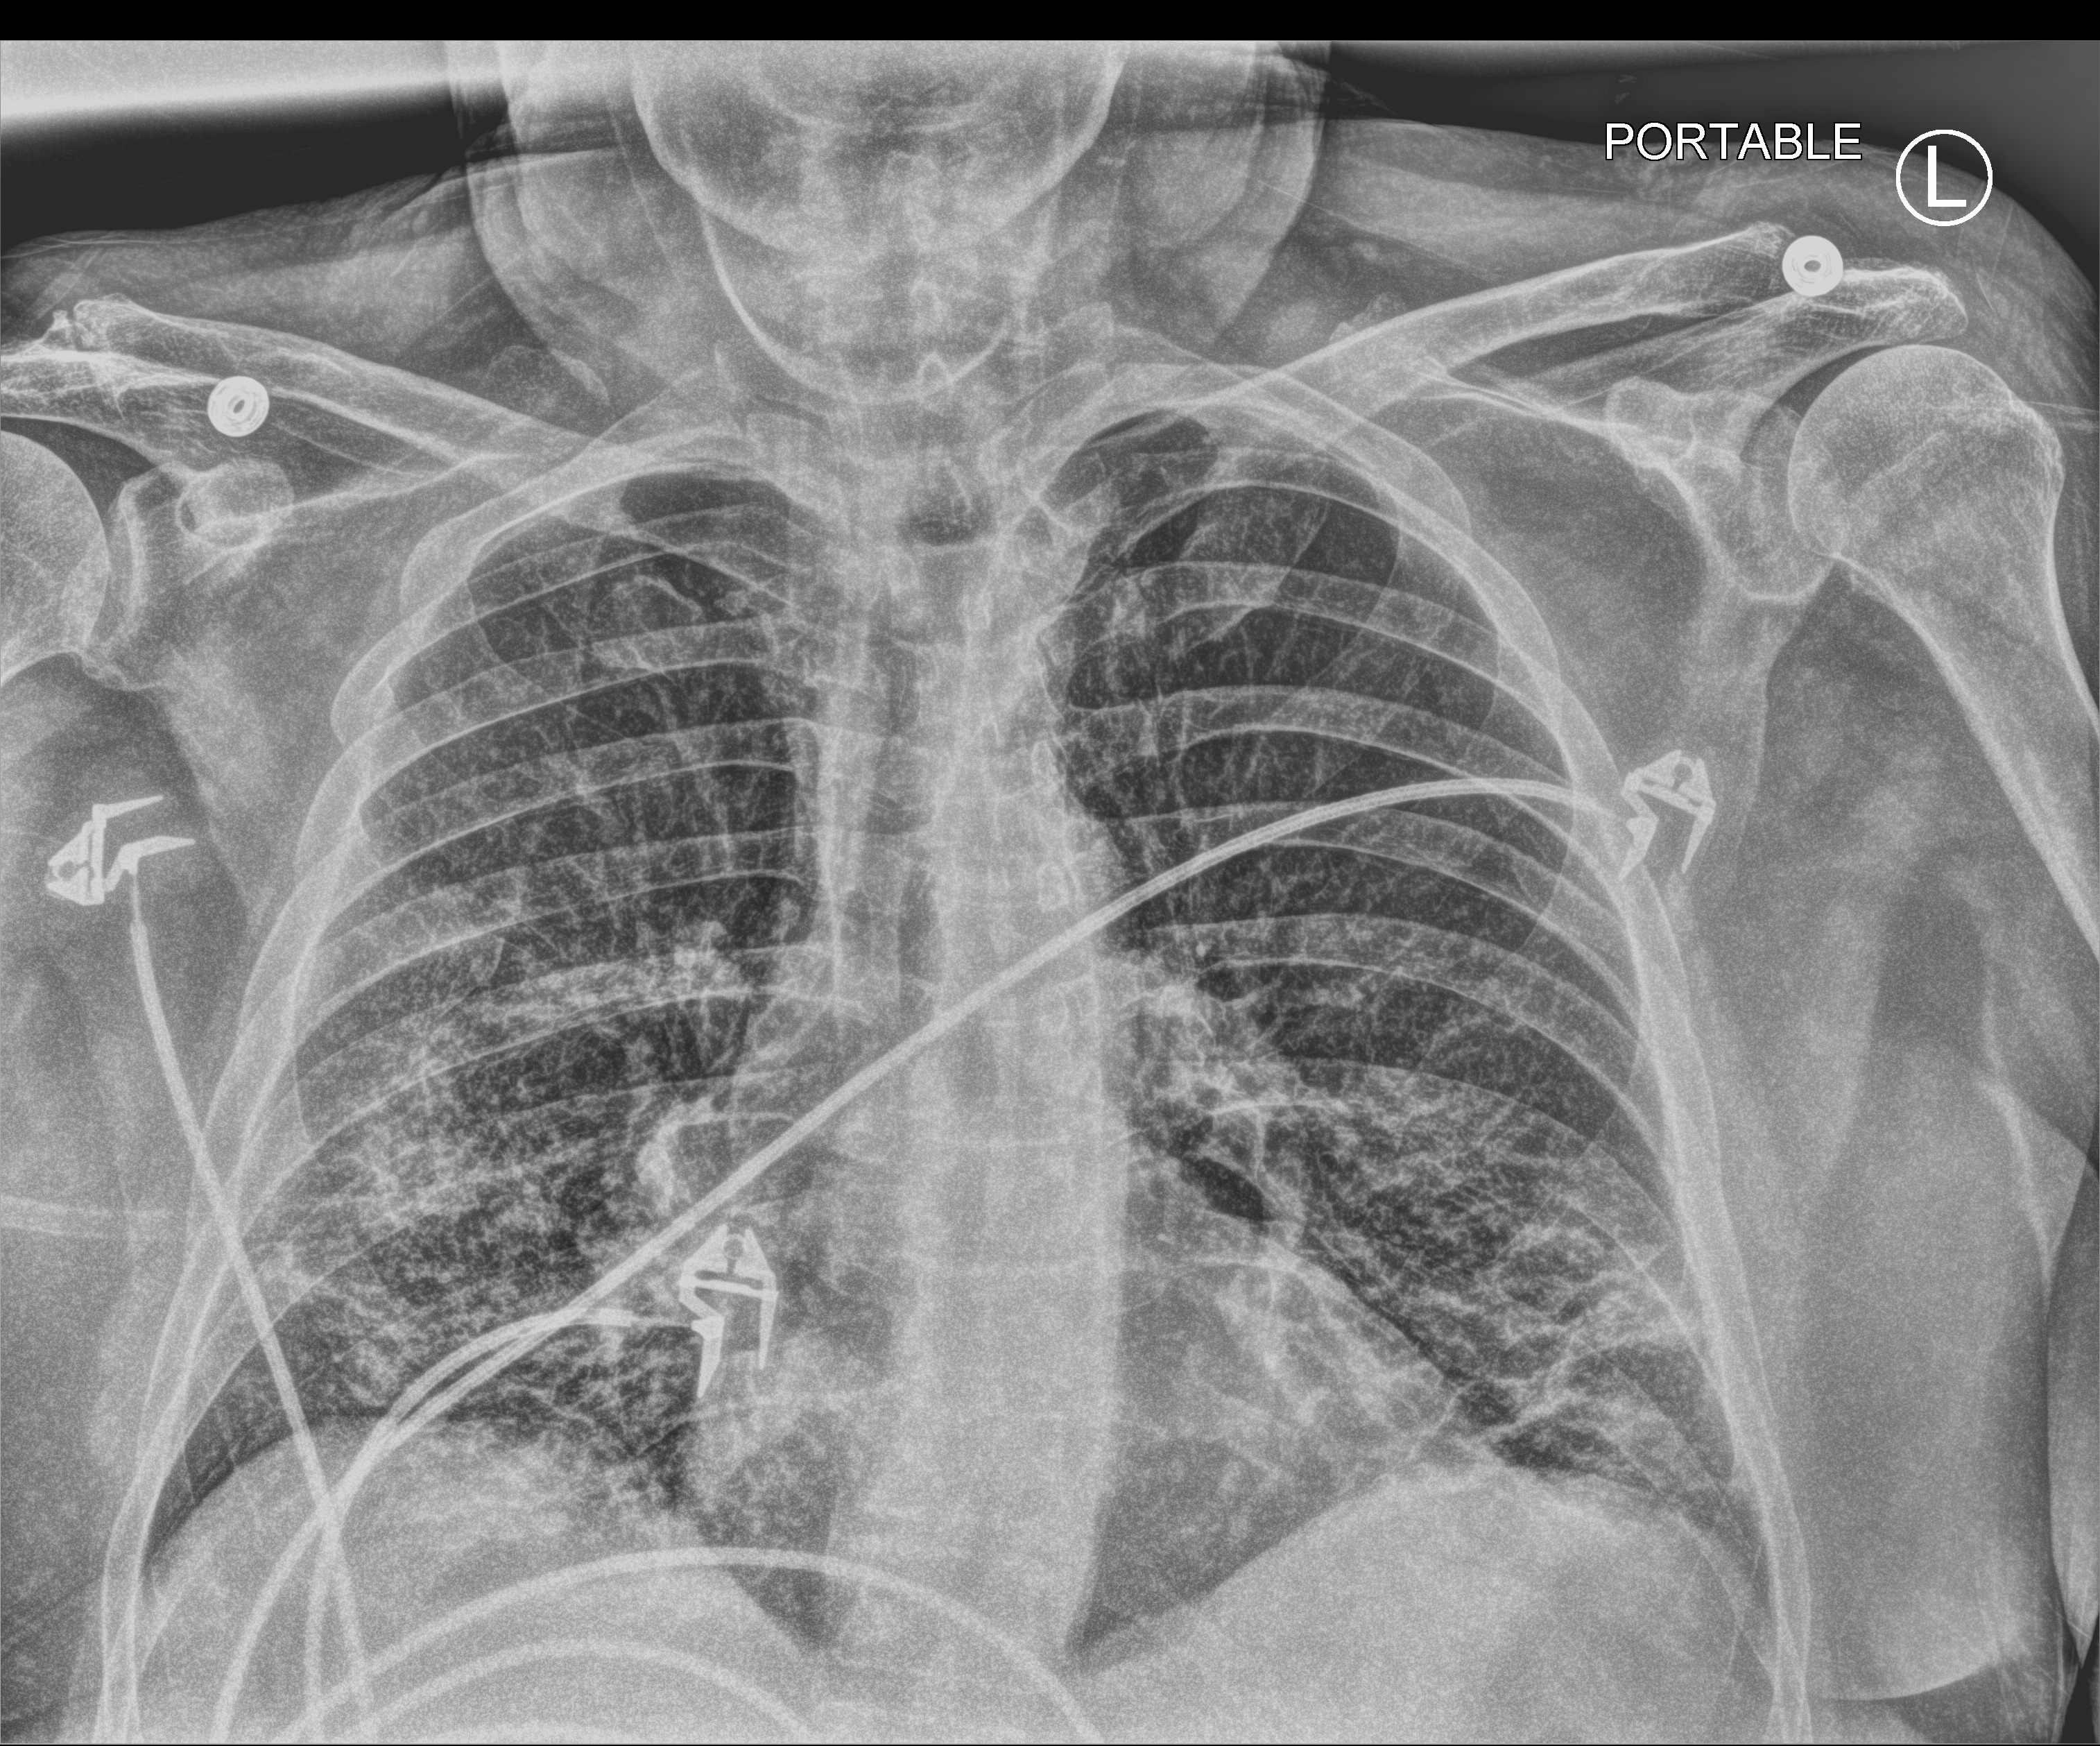
Bedside chest radiograph (computed radiography), anteroposterior (AP) projection. Male patient hospitalised with COVID-19, age 60–74 years.
Admission-level facts for this patient (not findings on this image; timing relative to this image not recorded):
- mechanically ventilated during this hospital stay: no
- chronic kidney disease (admission record): no